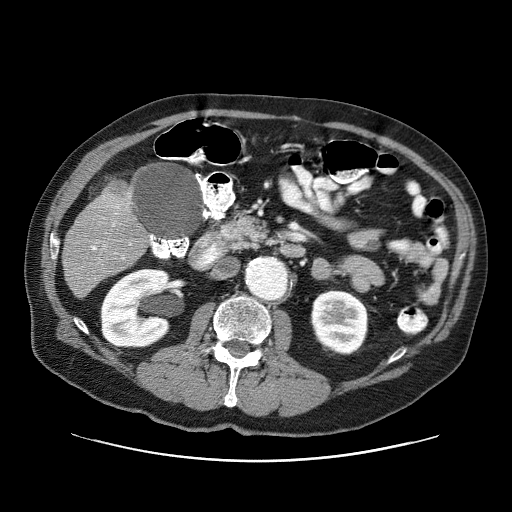
Contrast-enhanced abdominal CT (liver protocol), one axial slice; slice 17 of 87 in the series (ordered by position); reconstruction kernel STANDARD; 120 kVp; one of 3 acquisitions stored at this slice position; soft-tissue window (W 400 / L 40 HU); 2.5 mm slice thickness; 512 × 512 image matrix, field of view 400 × 400 mm. Case-level facts recorded for this patient, not image findings: diagnosis: hepatocellular carcinoma (patient treated with transarterial chemoembolisation; whether this scan precedes or follows treatment is not stated here); TNM stage (as recorded): Stage-IIIA; Child-Pugh class: A; tumour differentiation: well differentiated; tumour nodularity: multinodular.
Annotated regions visible in this slice (semi-automatically segmented with operator editing):
- liver parenchyma outside the tumour (the mass and vessels are separate outlines, so this box may not span the whole liver): box from (x=62, y=187) to (x=146, y=298) px
- mass: (x=100, y=178)–(x=133, y=211)
- liver vessels: (x=91, y=208)–(x=131, y=258)